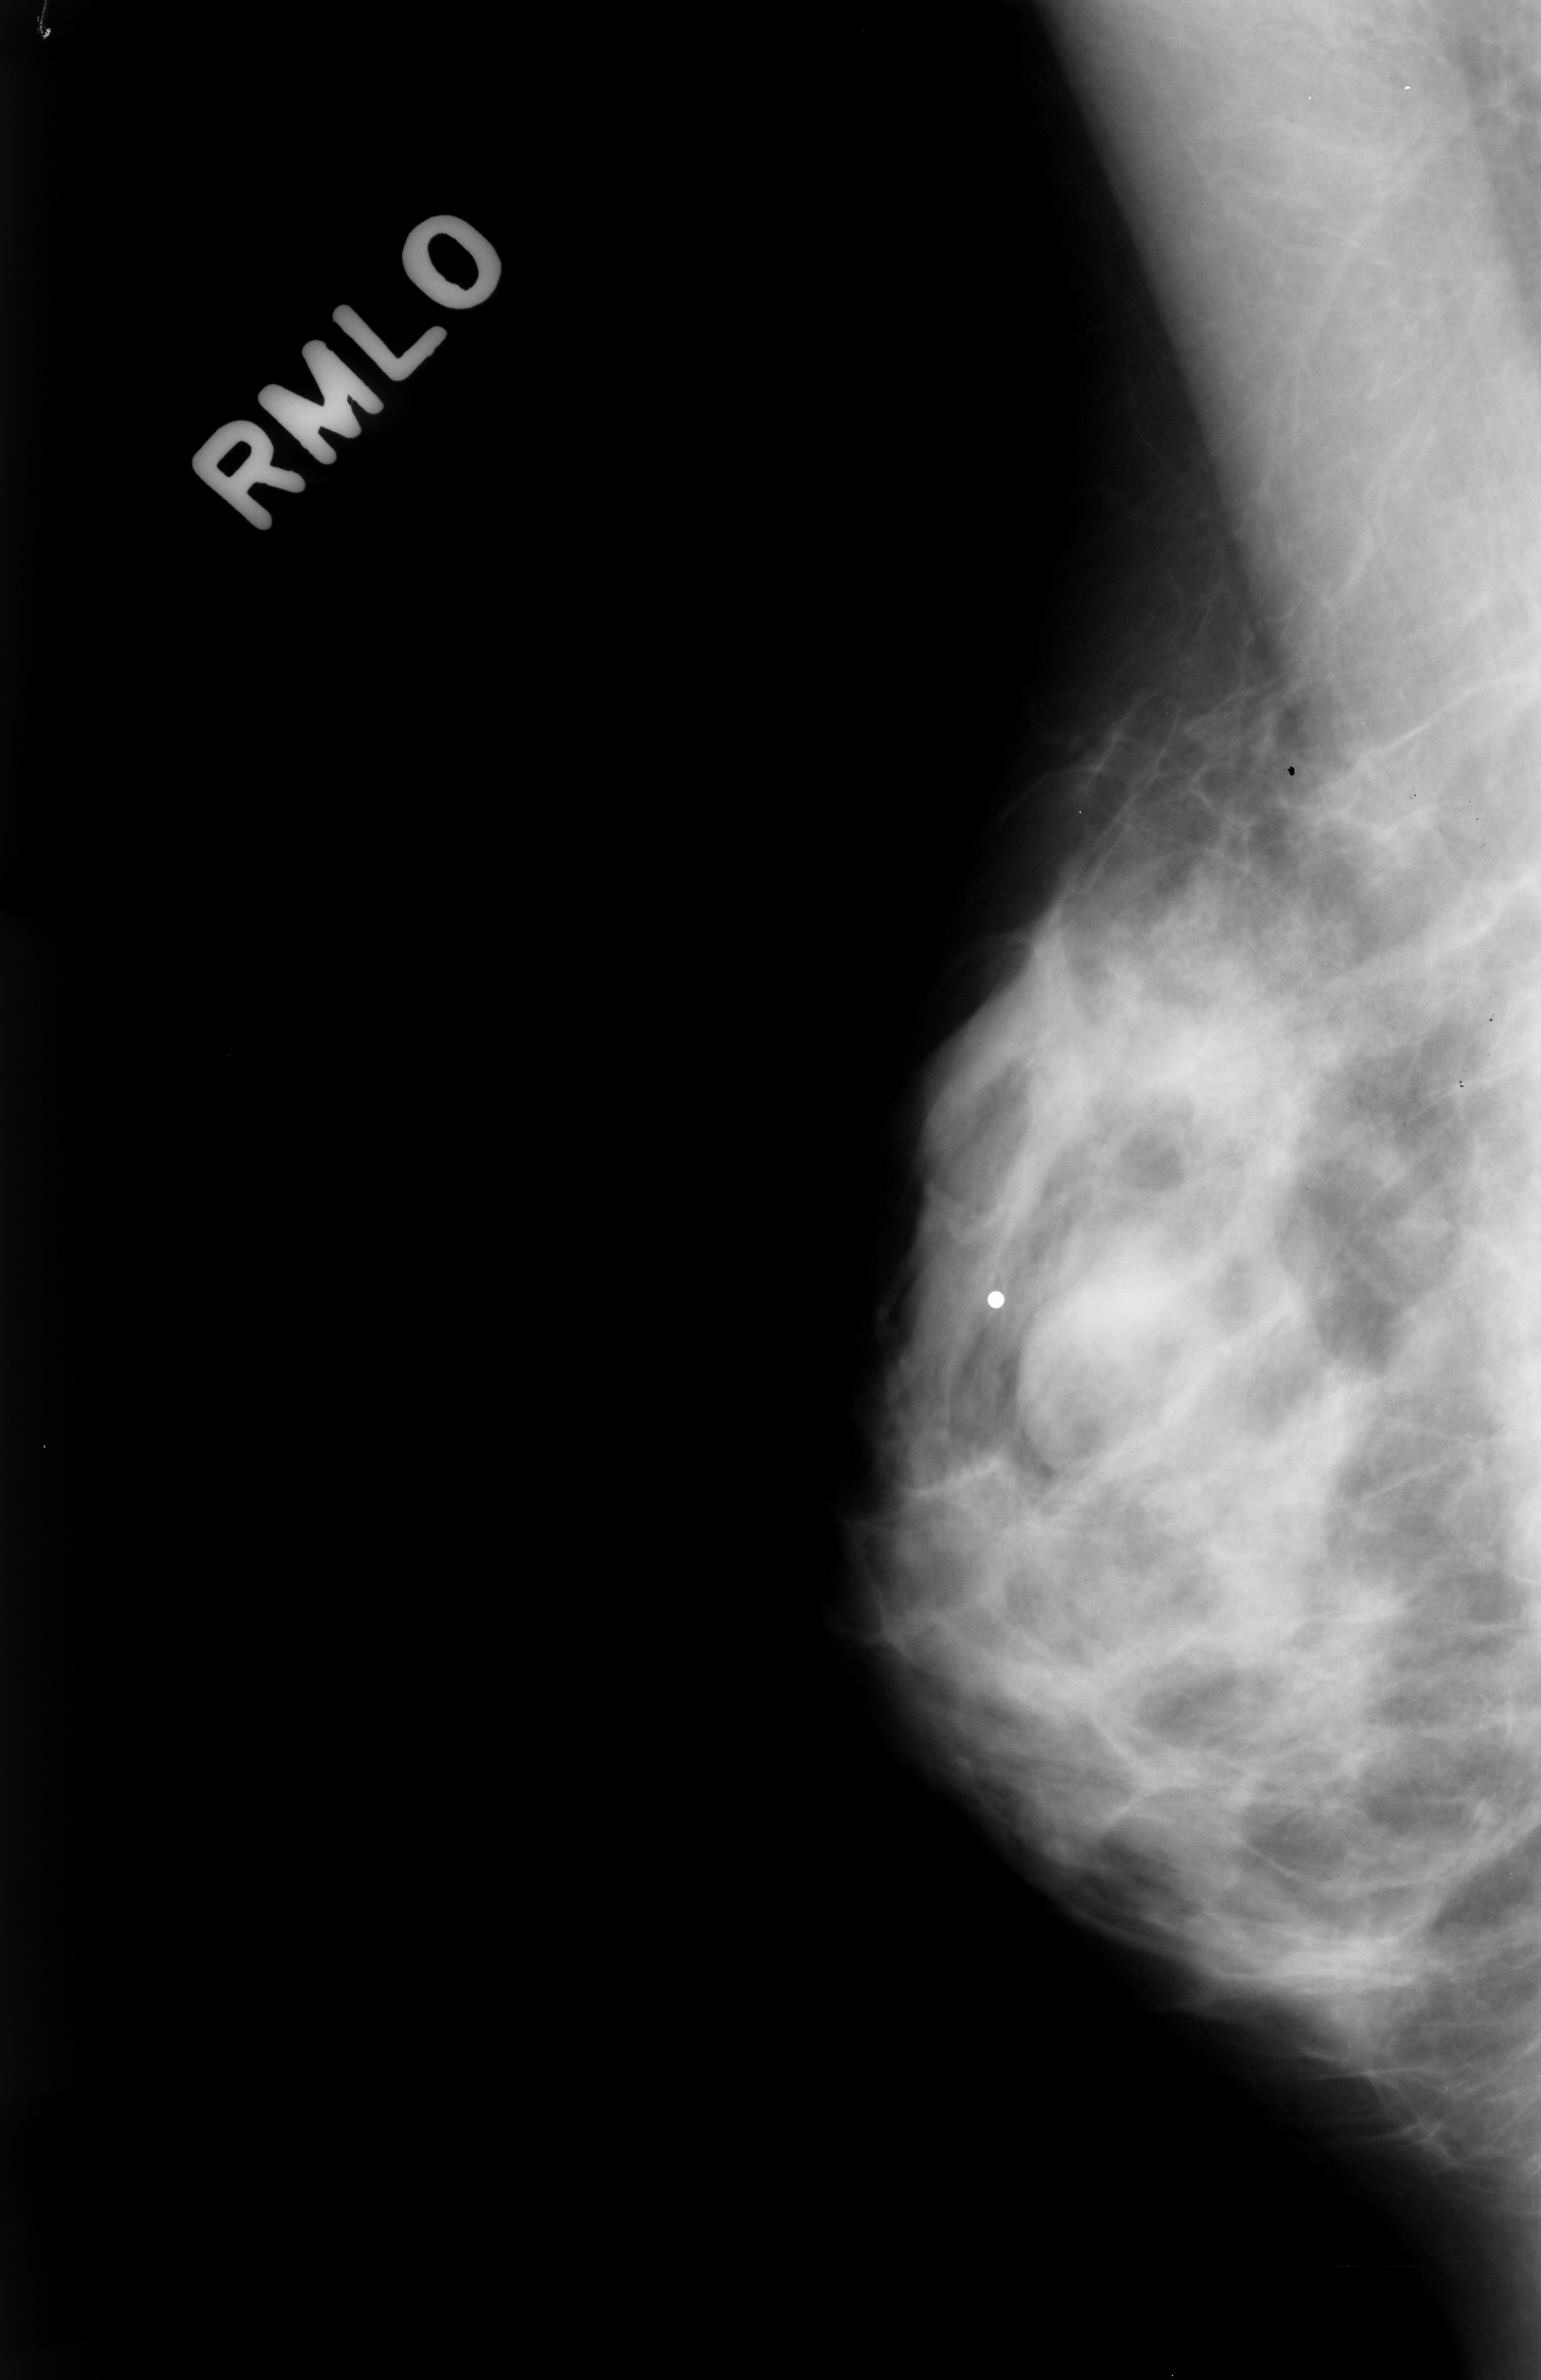
Mammogram (digitized film); right breast; mediolateral oblique (MLO) view; BI-RADS breast density category 3 (scale 1–4).
Marked findings (only marked abnormalities are described; nothing is implied about the rest of the image): mass, shape oval, margins obscured; BI-RADS assessment category 3; subtlety rating 4 on a 1 (subtle) to 5 (obvious) scale; pathology result (as recorded, not read from the image): benign.